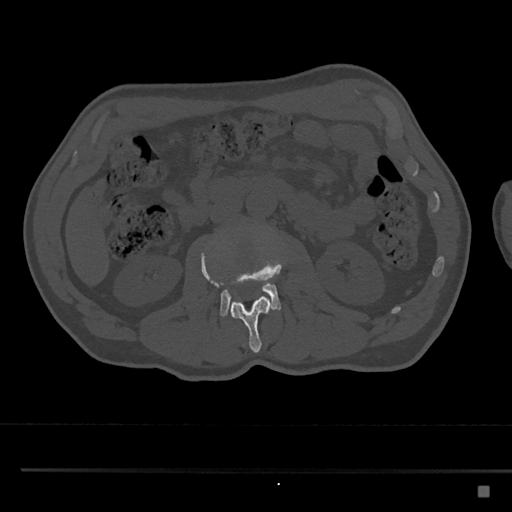
CT including the spine, one axial slice; slice 734 of 797 in the series (ordered by position); bone window (W 1800 / L 400 HU); 0.5 mm slice thickness; 512 × 512 image matrix, field of view 391 × 391 mm. Patient: male, 59 years. Case-level facts recorded for this patient, not image findings: primary cancer: prostate.
Annotated regions visible in this slice (semi-automatically segmented with operator editing):
- L2 vertebra: bounding box [x1, y1, x2, y2] px = [201, 236, 282, 353]
- L3 vertebra: [201, 229, 281, 318]